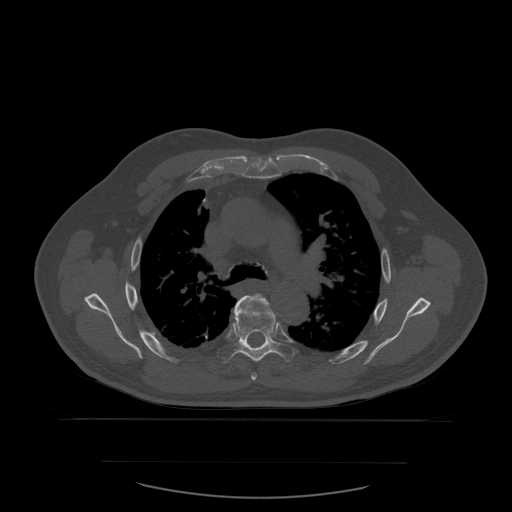
CT including the spine, one axial slice. Slice 409 of 590 in the series (ordered by position). Bone window (W 1800 / L 400 HU). 512 × 512 image matrix. Patient age 71 years. Case-level facts recorded for this patient, not image findings: primary cancer: lung; vertebrae with lytic lesions (as recorded): T1, T2, L5, S1.
Annotated regions visible in this slice (semi-automatic segmentation, software-assisted and operator-edited):
- T5 vertebra: box from (x=236, y=294) to (x=274, y=381) px
- T6 vertebra: (x=217, y=296)–(x=295, y=364)